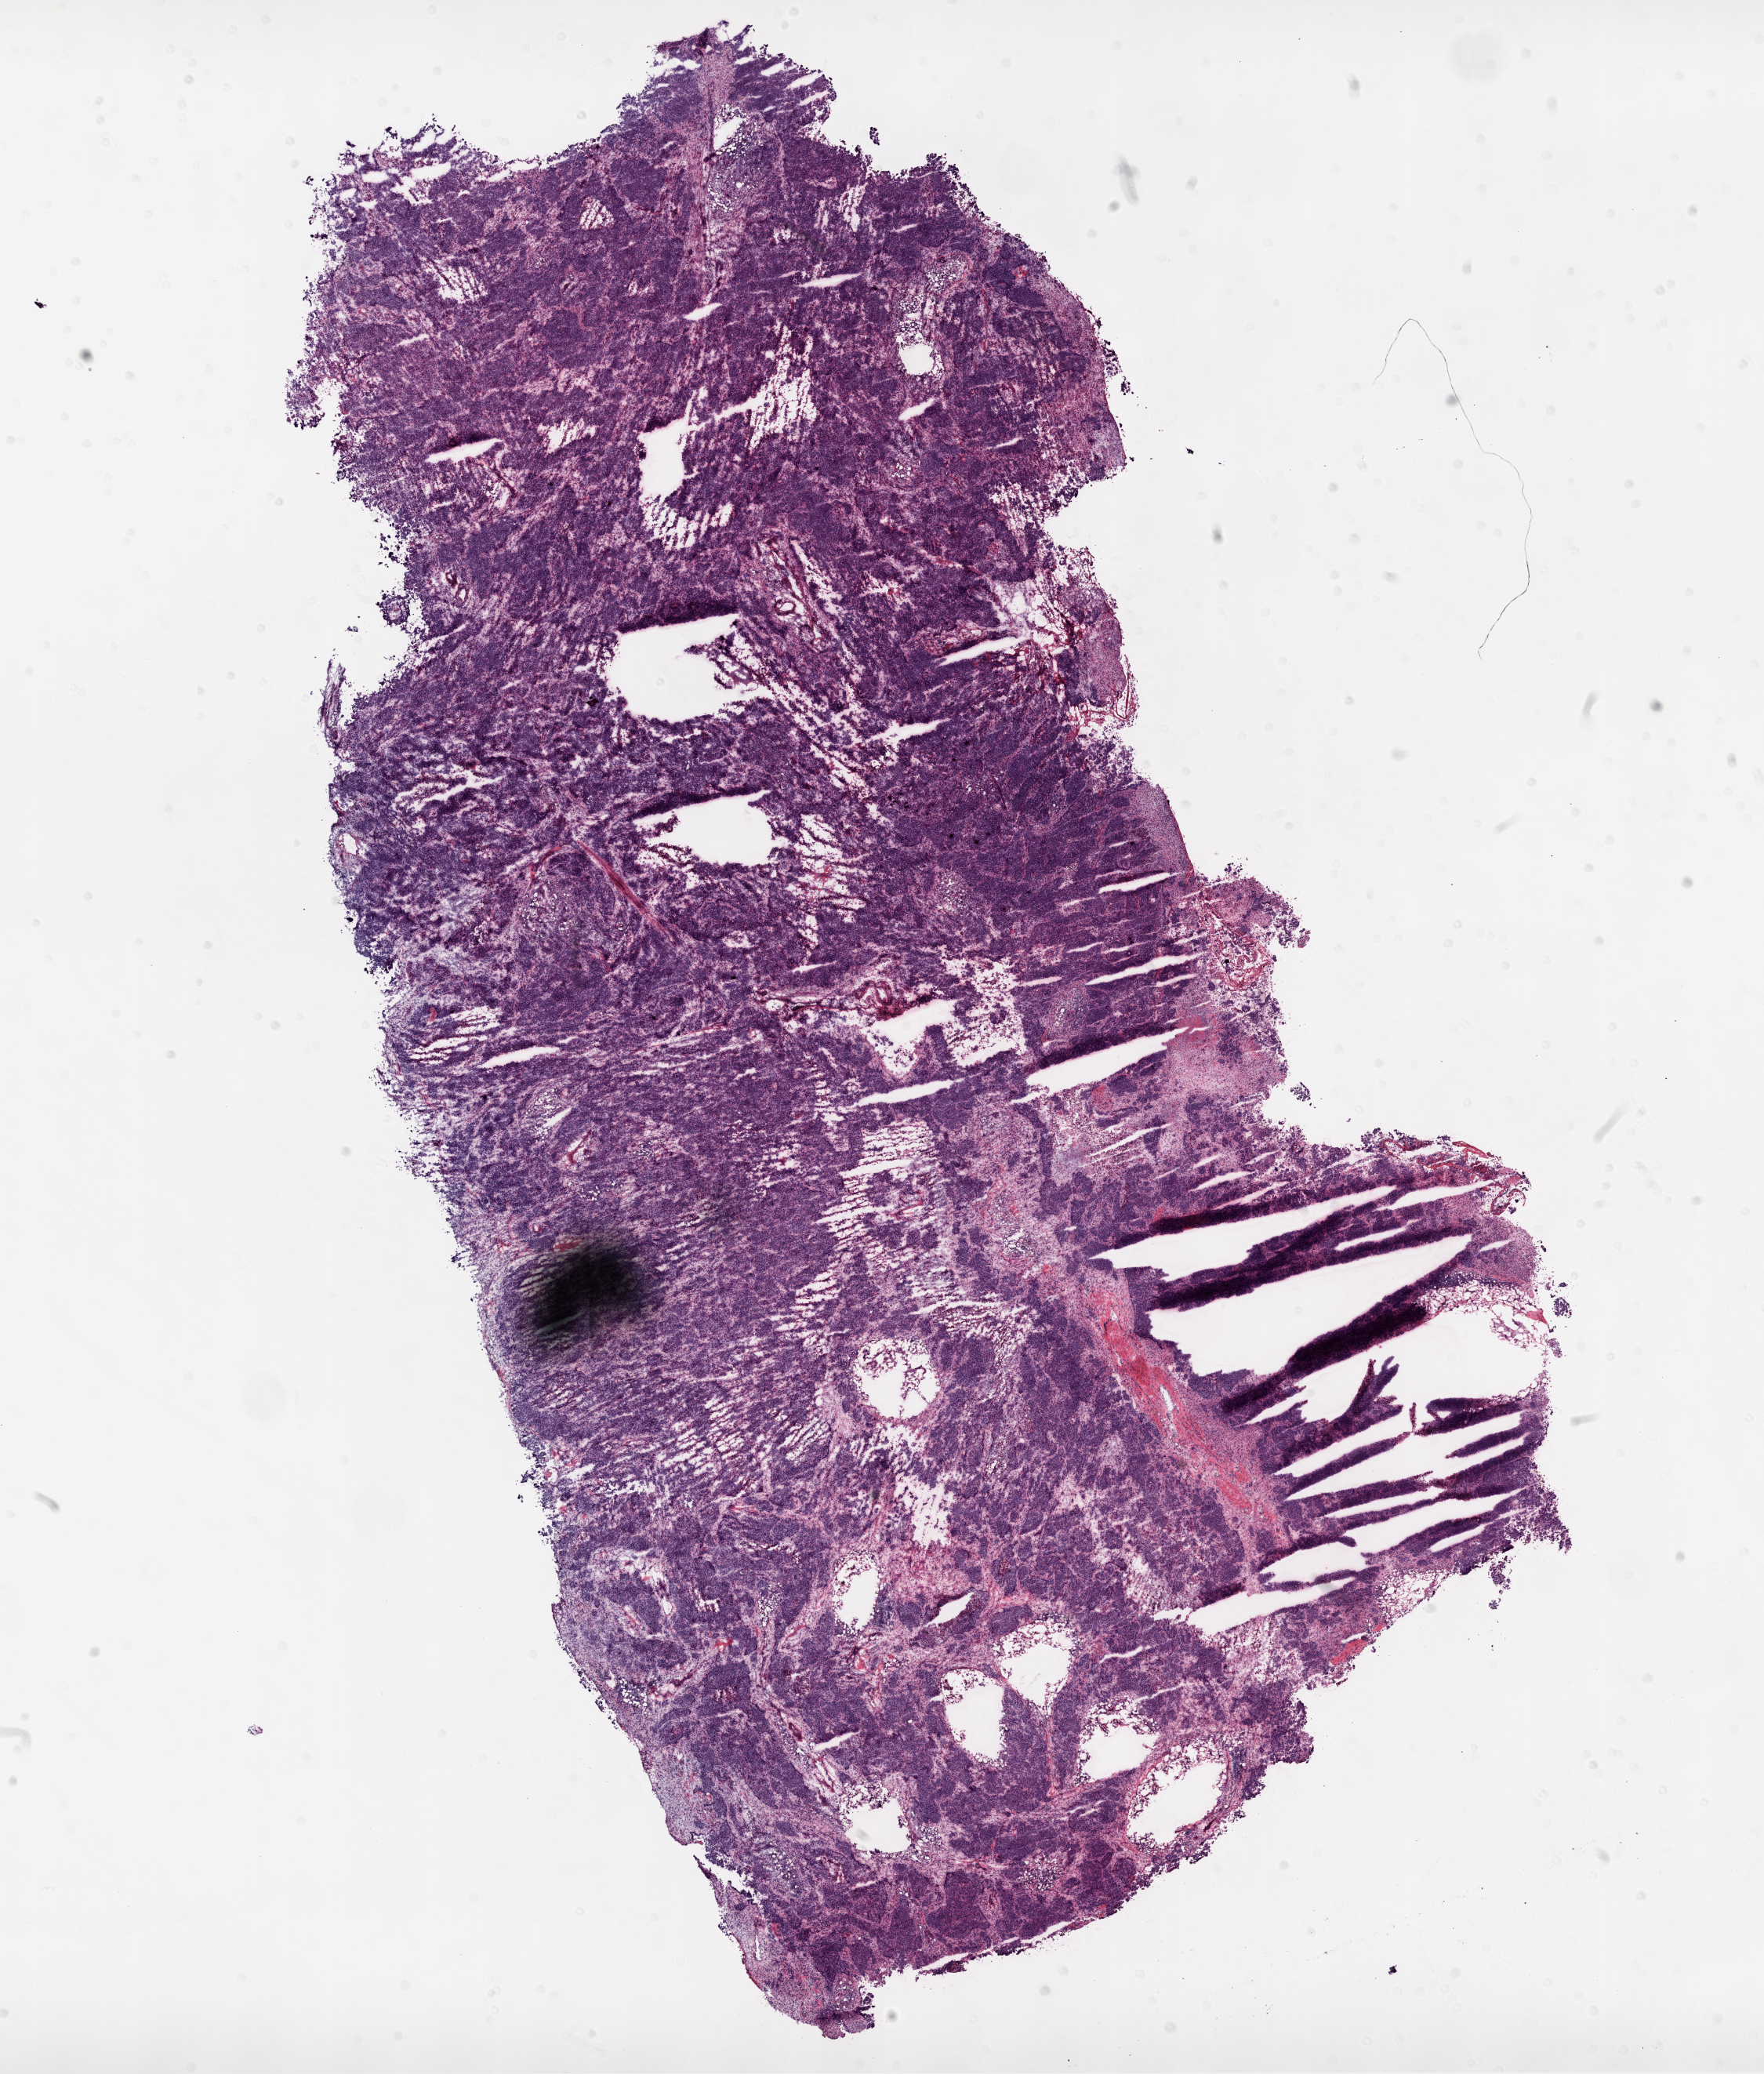
Whole-slide histology image, H&E-stained — whole scanned area (about 18.1 x 21.2 mm, slide scanned at 20x) shown as a low-resolution overview. Frozen section from the top of the tissue portion. Primary tumour sample from the ovary. Female, age 77 years at initial diagnosis. Histologic grade: G3 (poorly differentiated). Pathologist review of this section (percent, as recorded): tumour cells 90%, tumour nuclei 95%, normal cells 0%, stromal cells 5%, necrosis 5%.
Diagnosis: Serous cystadenocarcinoma, NOS. FIGO stage: IIIC.